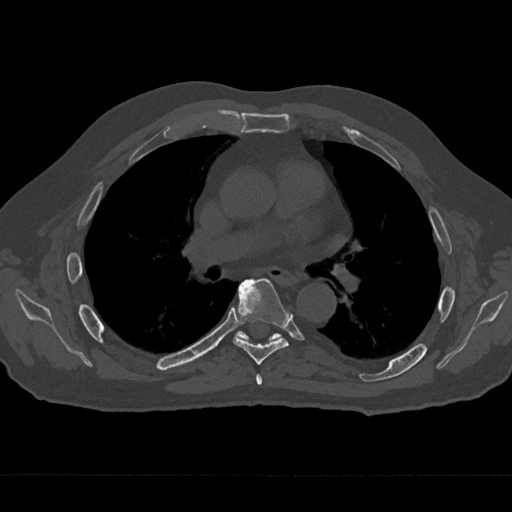
CT including the spine, one axial slice. Position 410 of 797 along the scan axis. Reconstruction kernel Br40s/3. Bone window (W 1800 / L 400 HU). 512 × 512 image matrix, field of view 377 × 377 mm. Male patient, age 75 years. From the clinical record (not read from this slice): primary cancer: renal; vertebrae with lytic lesions (as recorded): T4.
Annotated regions visible in this slice (semi-automatically segmented with operator editing):
- T5 vertebra: bounding box (x1, y1, x2, y2) in pixels: (256, 374, 263, 385)
- T6 vertebra: (233, 278, 289, 365)
- T7 vertebra: (237, 331, 280, 341)